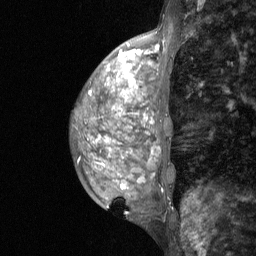
Breast MRI (dynamic contrast-enhanced), one sagittal slice. Position 21 of 64 along the scan axis. Dynamic contrast-enhanced study with each time point stored as its own series, time point 2 of 3 at this slice position (early post-contrast, ordered by acquisition time). 1.5 T. TE 4.8 ms, TR 27 ms. 256 × 256 image matrix, field of view 200 × 200 mm. Female patient, age 36 years. Case-level facts recorded for this patient, not image findings: setting: breast cancer imaged before/during neoadjuvant chemotherapy; receptor status: HR-positive, HER2-negative.
Structures marked on this image (semi-automatically segmented with operator editing):
- analysis volume of interest (the breast-tissue region the enhancement analysis was run in; not a lesion): bounding box (x1, y1, x2, y2) in pixels: (73, 63, 174, 209)
- tumour enhancement mask (voxels above the 90 % enhancement threshold inside the analysis volume of interest): (121, 64, 131, 188)